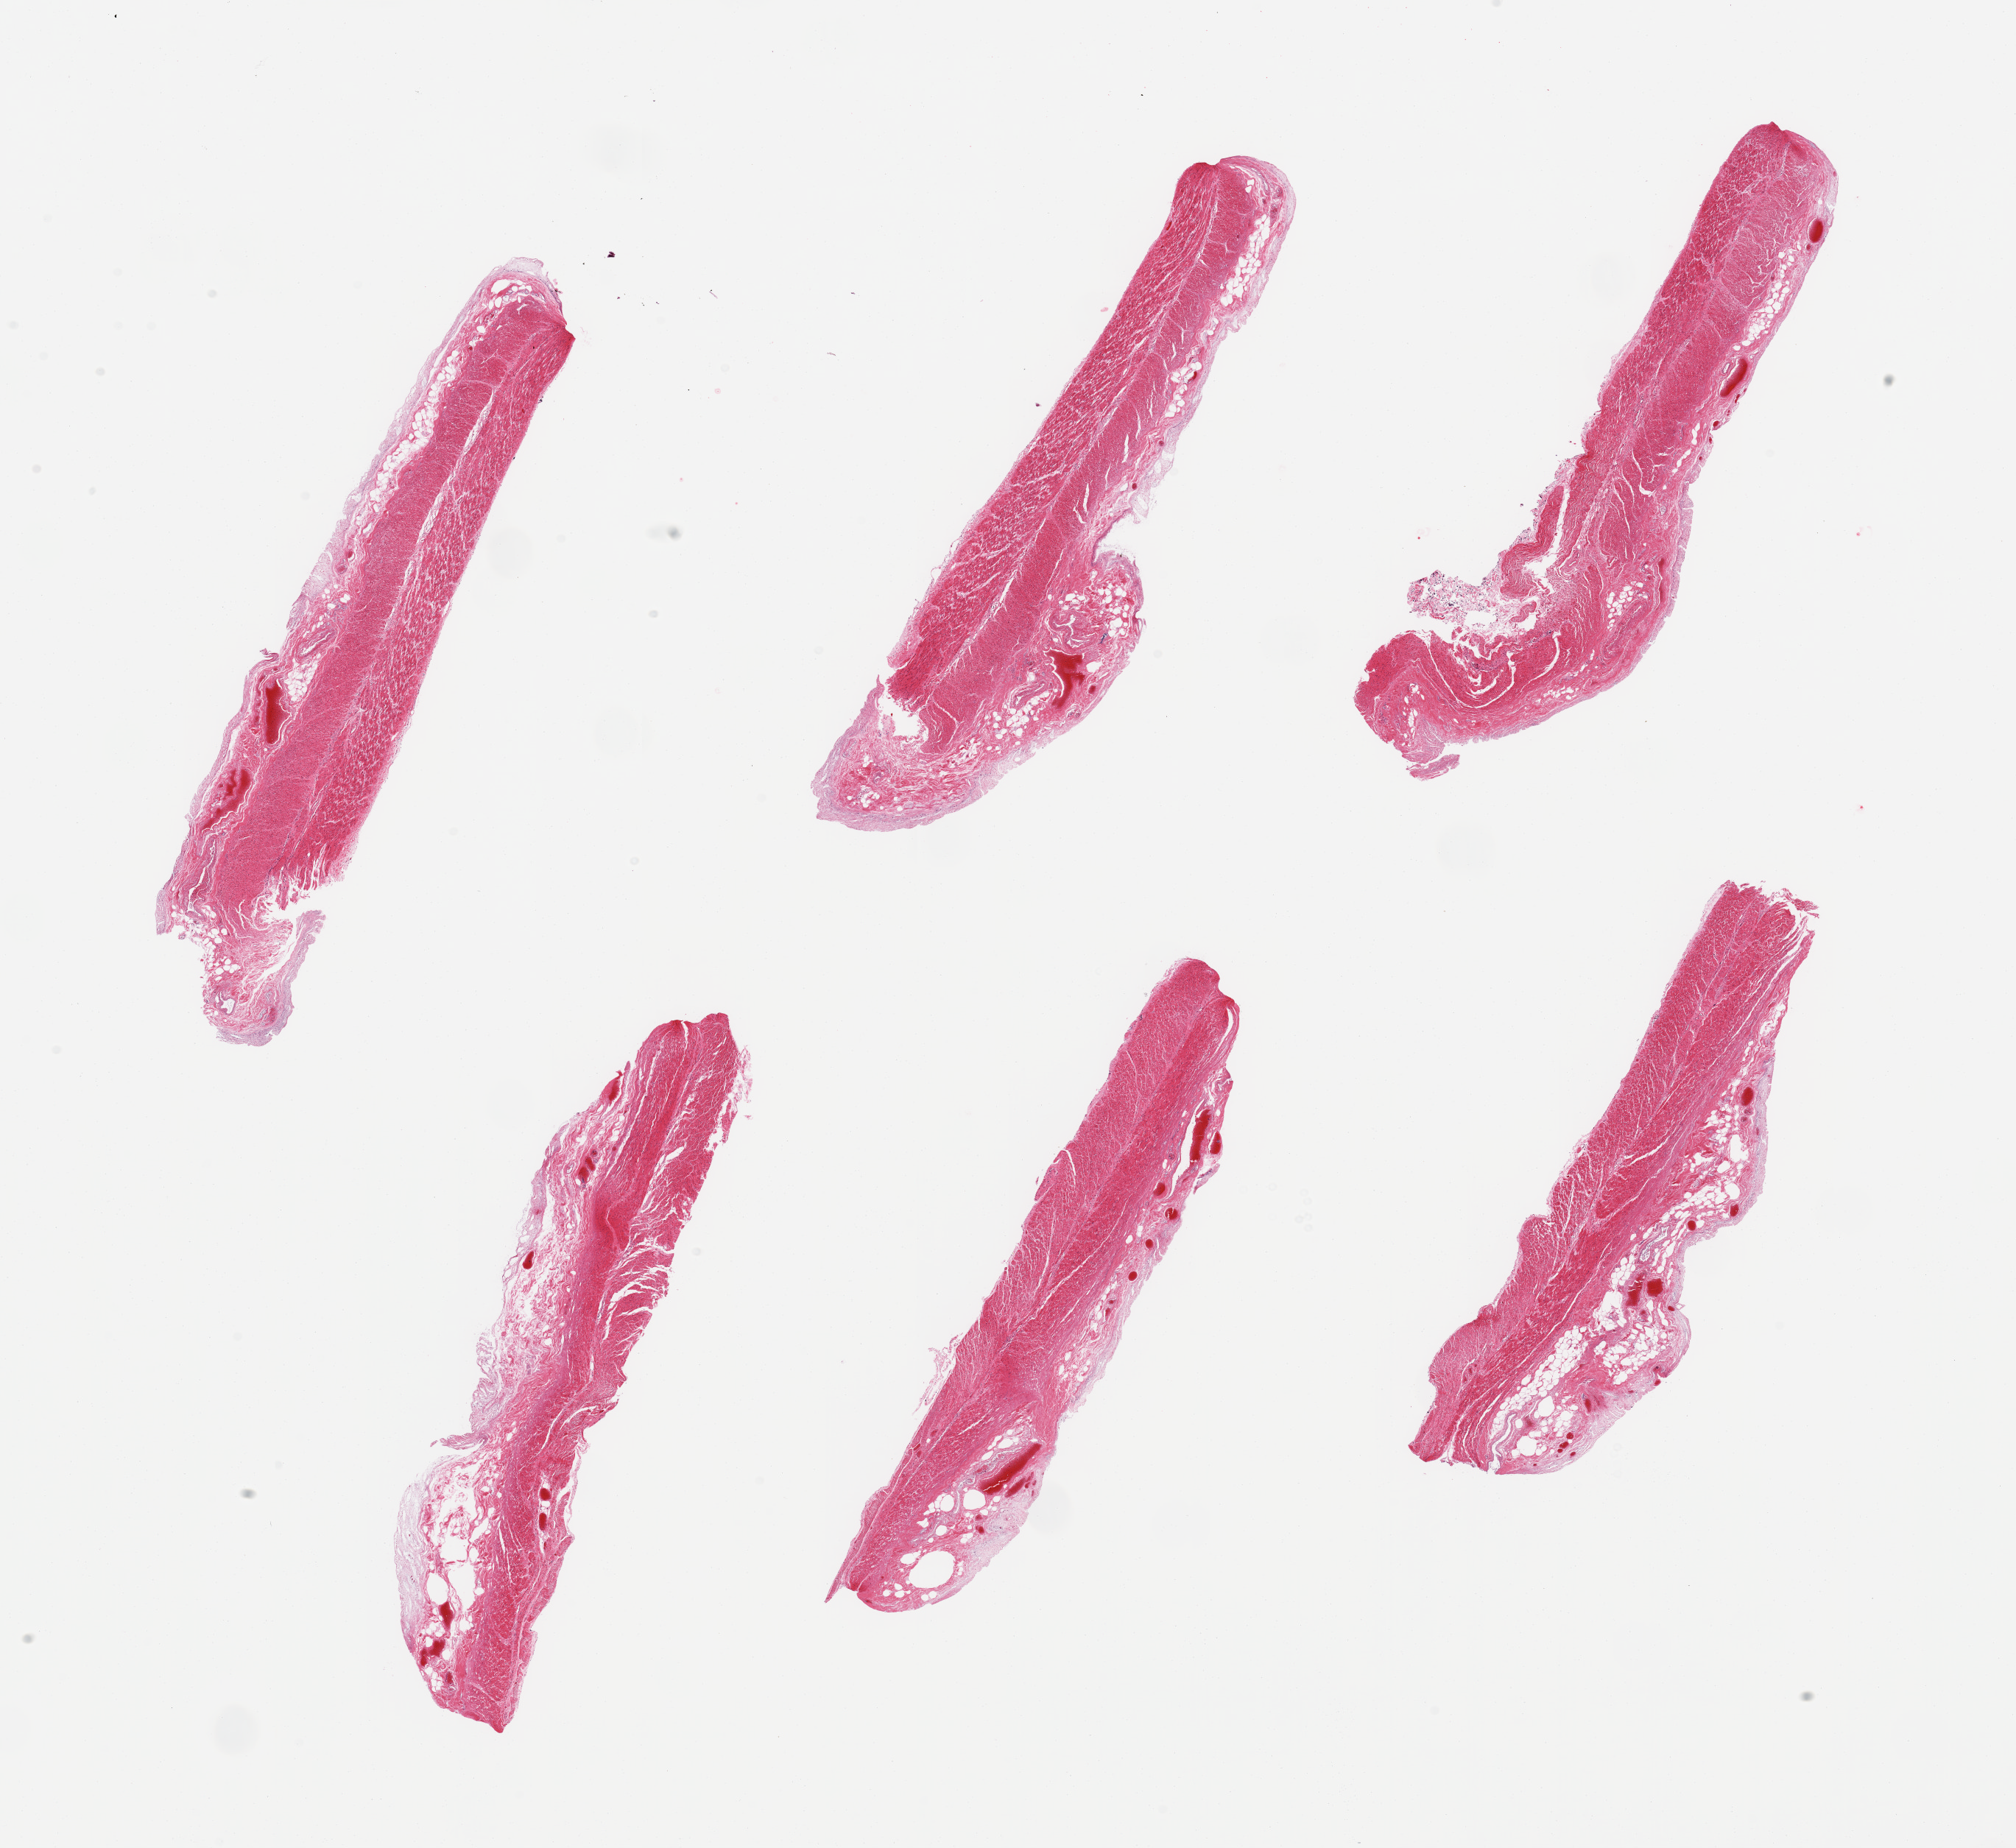
Hematoxylin and eosin (H&E) whole-slide image, whole scanned area (about 21.7 x 19.9 mm, slide scanned at 20x) shown as a low-resolution overview. PAXgene-fixed, paraffin-embedded tissue. Sampled site (target tissue): transverse colon. Tissue donor sample. Donor sex: male.
Pathologist's review note for this sample: 6 pieces; no mucosa; could be used to compare with sigmoid colon.